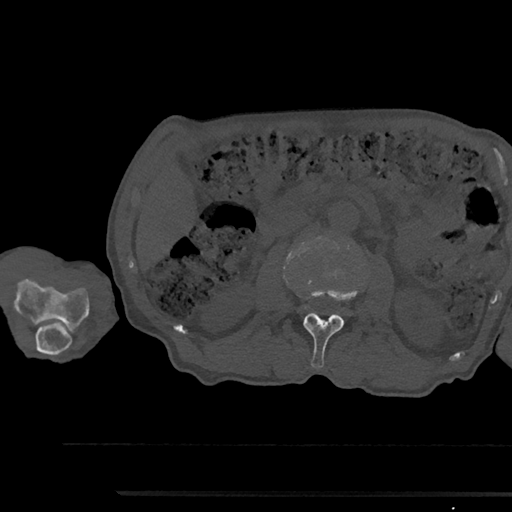
CT including the spine, one axial slice; position 541 of 797 along the scan axis; reconstruction kernel Br40s/3; 120 kVp; bone window (W 1800 / L 400 HU); 0.5 mm slice thickness; 512 × 512 image matrix, field of view 367 × 367 mm. Male patient, age 79 years. From the clinical record (not read from this slice): primary cancer: prostate.
Structures marked on this image (semi-automatic segmentation, software-assisted and operator-edited):
- L2 vertebra: box from (x=303, y=289) to (x=358, y=368) px